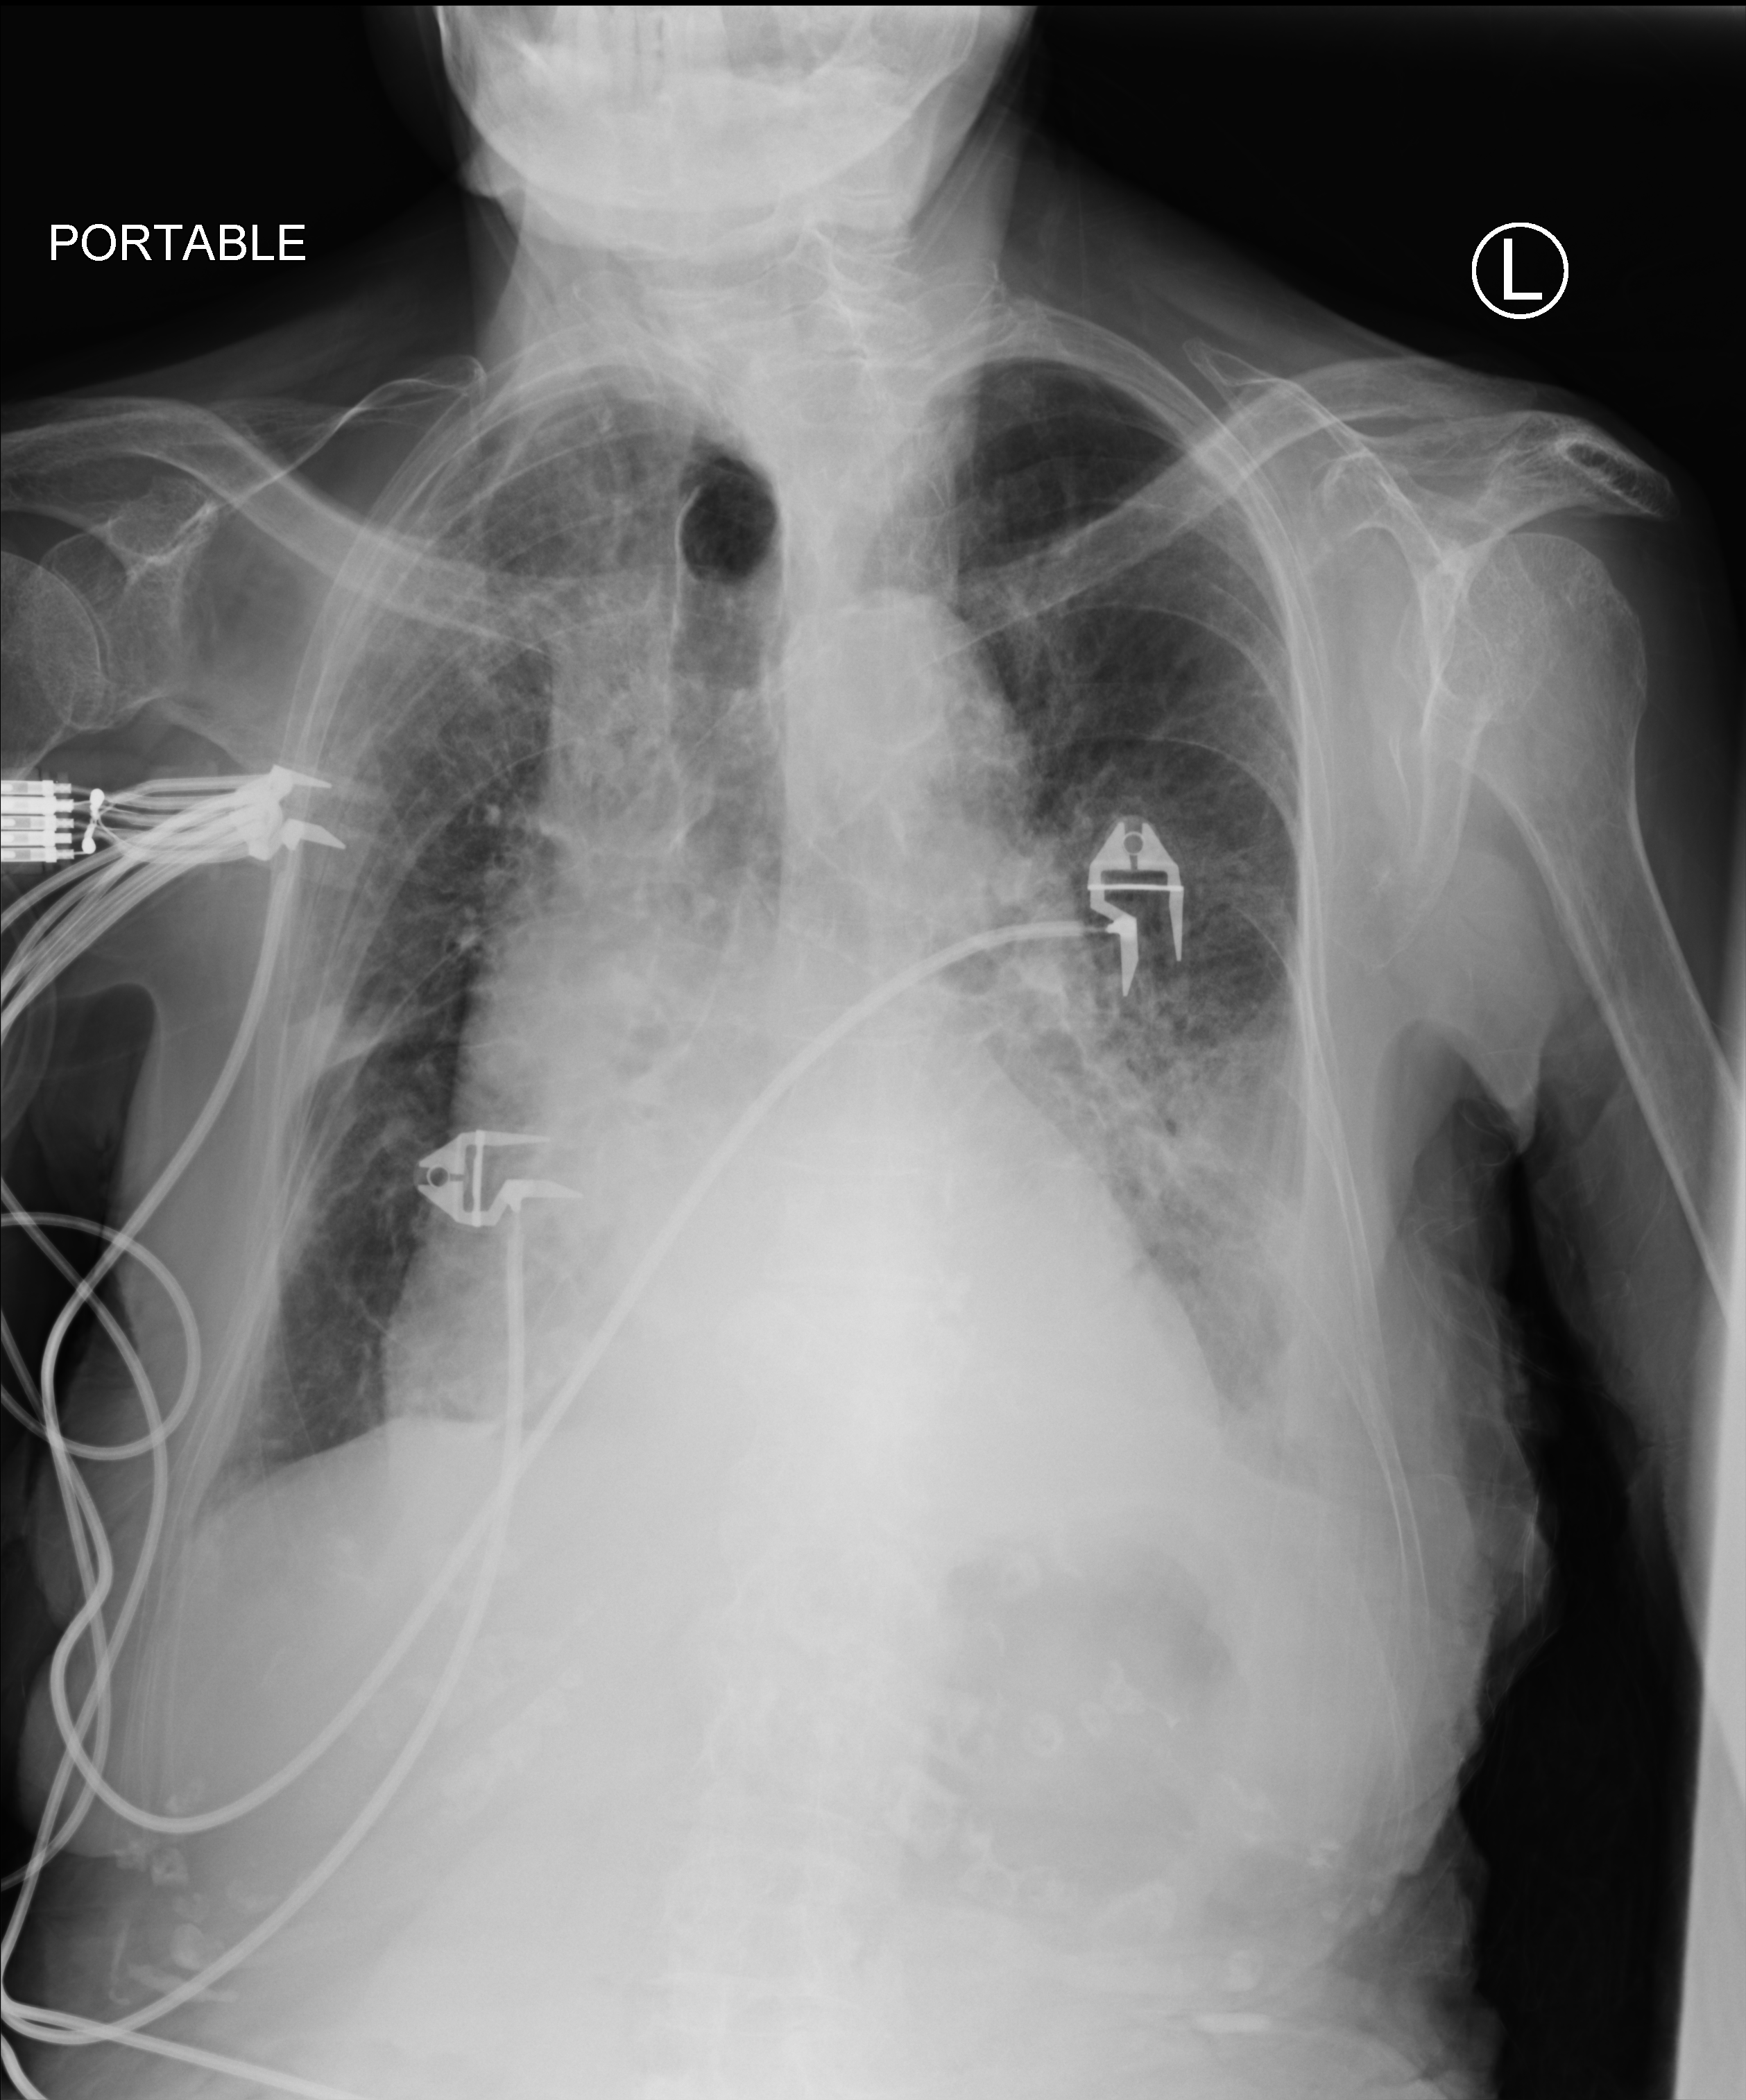
Portable chest radiograph; anteroposterior (AP) projection. Patient hospitalised with COVID-19; female, aged 75–90 years.
From the hospital-stay record, not from the radiograph (when in the stay this image was taken is not recorded): admitted to intensive care during this hospital stay: no; mechanically ventilated during this hospital stay: no.